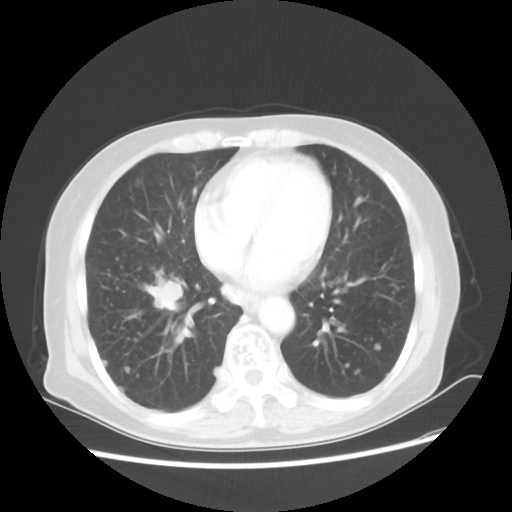
Chest CT, one axial slice; slice 21 of 56 in the series (ordered by position); 80 kVp; lung window (W 1500 / L -600 HU); 512 × 512 image matrix. Female patient, age 68 years. Case-level facts recorded for this patient, not image findings: clinical TNM (as recorded): T1c N3 M0.
Annotated regions visible in this slice (bounding box drawn by a radiologist):
- lung tumour (recorded histology: squamous cell carcinoma): bounding box [x1, y1, x2, y2] px = [144, 274, 183, 324]